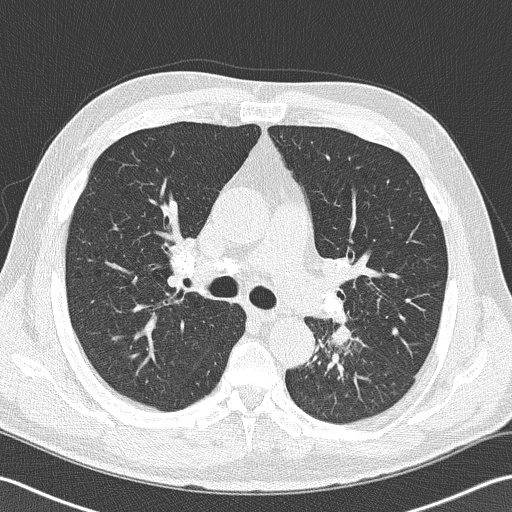
Low-dose screening chest CT, axial slice. Second screening round (one year after baseline). Lung window (W 1500 / L -600 HU). 2 mm slice thickness. Lung (sharp) reconstruction kernel (B50f). 512 × 512 image matrix. Male participant, aged 57 years at enrolment. Former smoker at enrolment.
- Expert reader's lesion annotation, bounding box [x1, y1, x2, y2] px = [294, 313, 375, 387].
- The exam's reader record, not a measurement of the box and not confirmed to be the same lesion: non-calcified nodule or mass ≥4 mm, left lower lobe, 40 × 30 mm, spiculated (stellate) margins, soft tissue attenuation, pre-existing on the prior screen: no.
- Later outcome: lung cancer diagnosed 9 days after this screen — squamous cell carcinoma, NOS, left lower lobe, moderately differentiated (G2), stage IIIB (AJCC 6th edition), 38 mm at pathology.